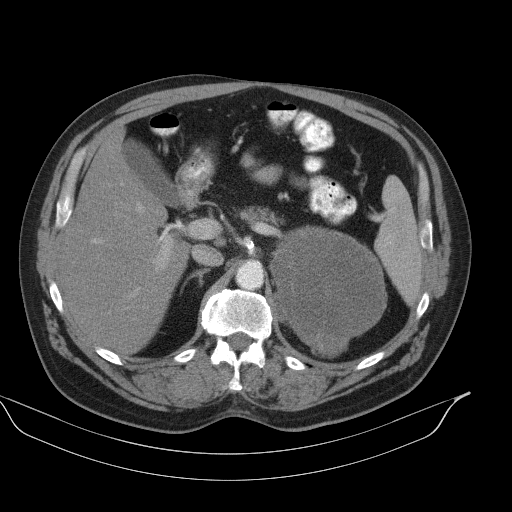
Contrast-enhanced abdominal CT, one axial slice; slice 68 of 92 in the series (ordered by position); 130 kVp; intravenous contrast given; soft-tissue window (W 400 / L 40 HU); 5 mm slice thickness; 512 × 512 image matrix. Patient: male, 56 years. Case-level facts recorded for this patient, not image findings: diagnosis: adrenocortical carcinoma; tumour side: left adrenal; tumour size at pathology: 15 cm.
Annotated regions visible in this slice (semi-automatic segmentation, software-assisted and operator-edited):
- mass: box from (x=272, y=227) to (x=387, y=356) px